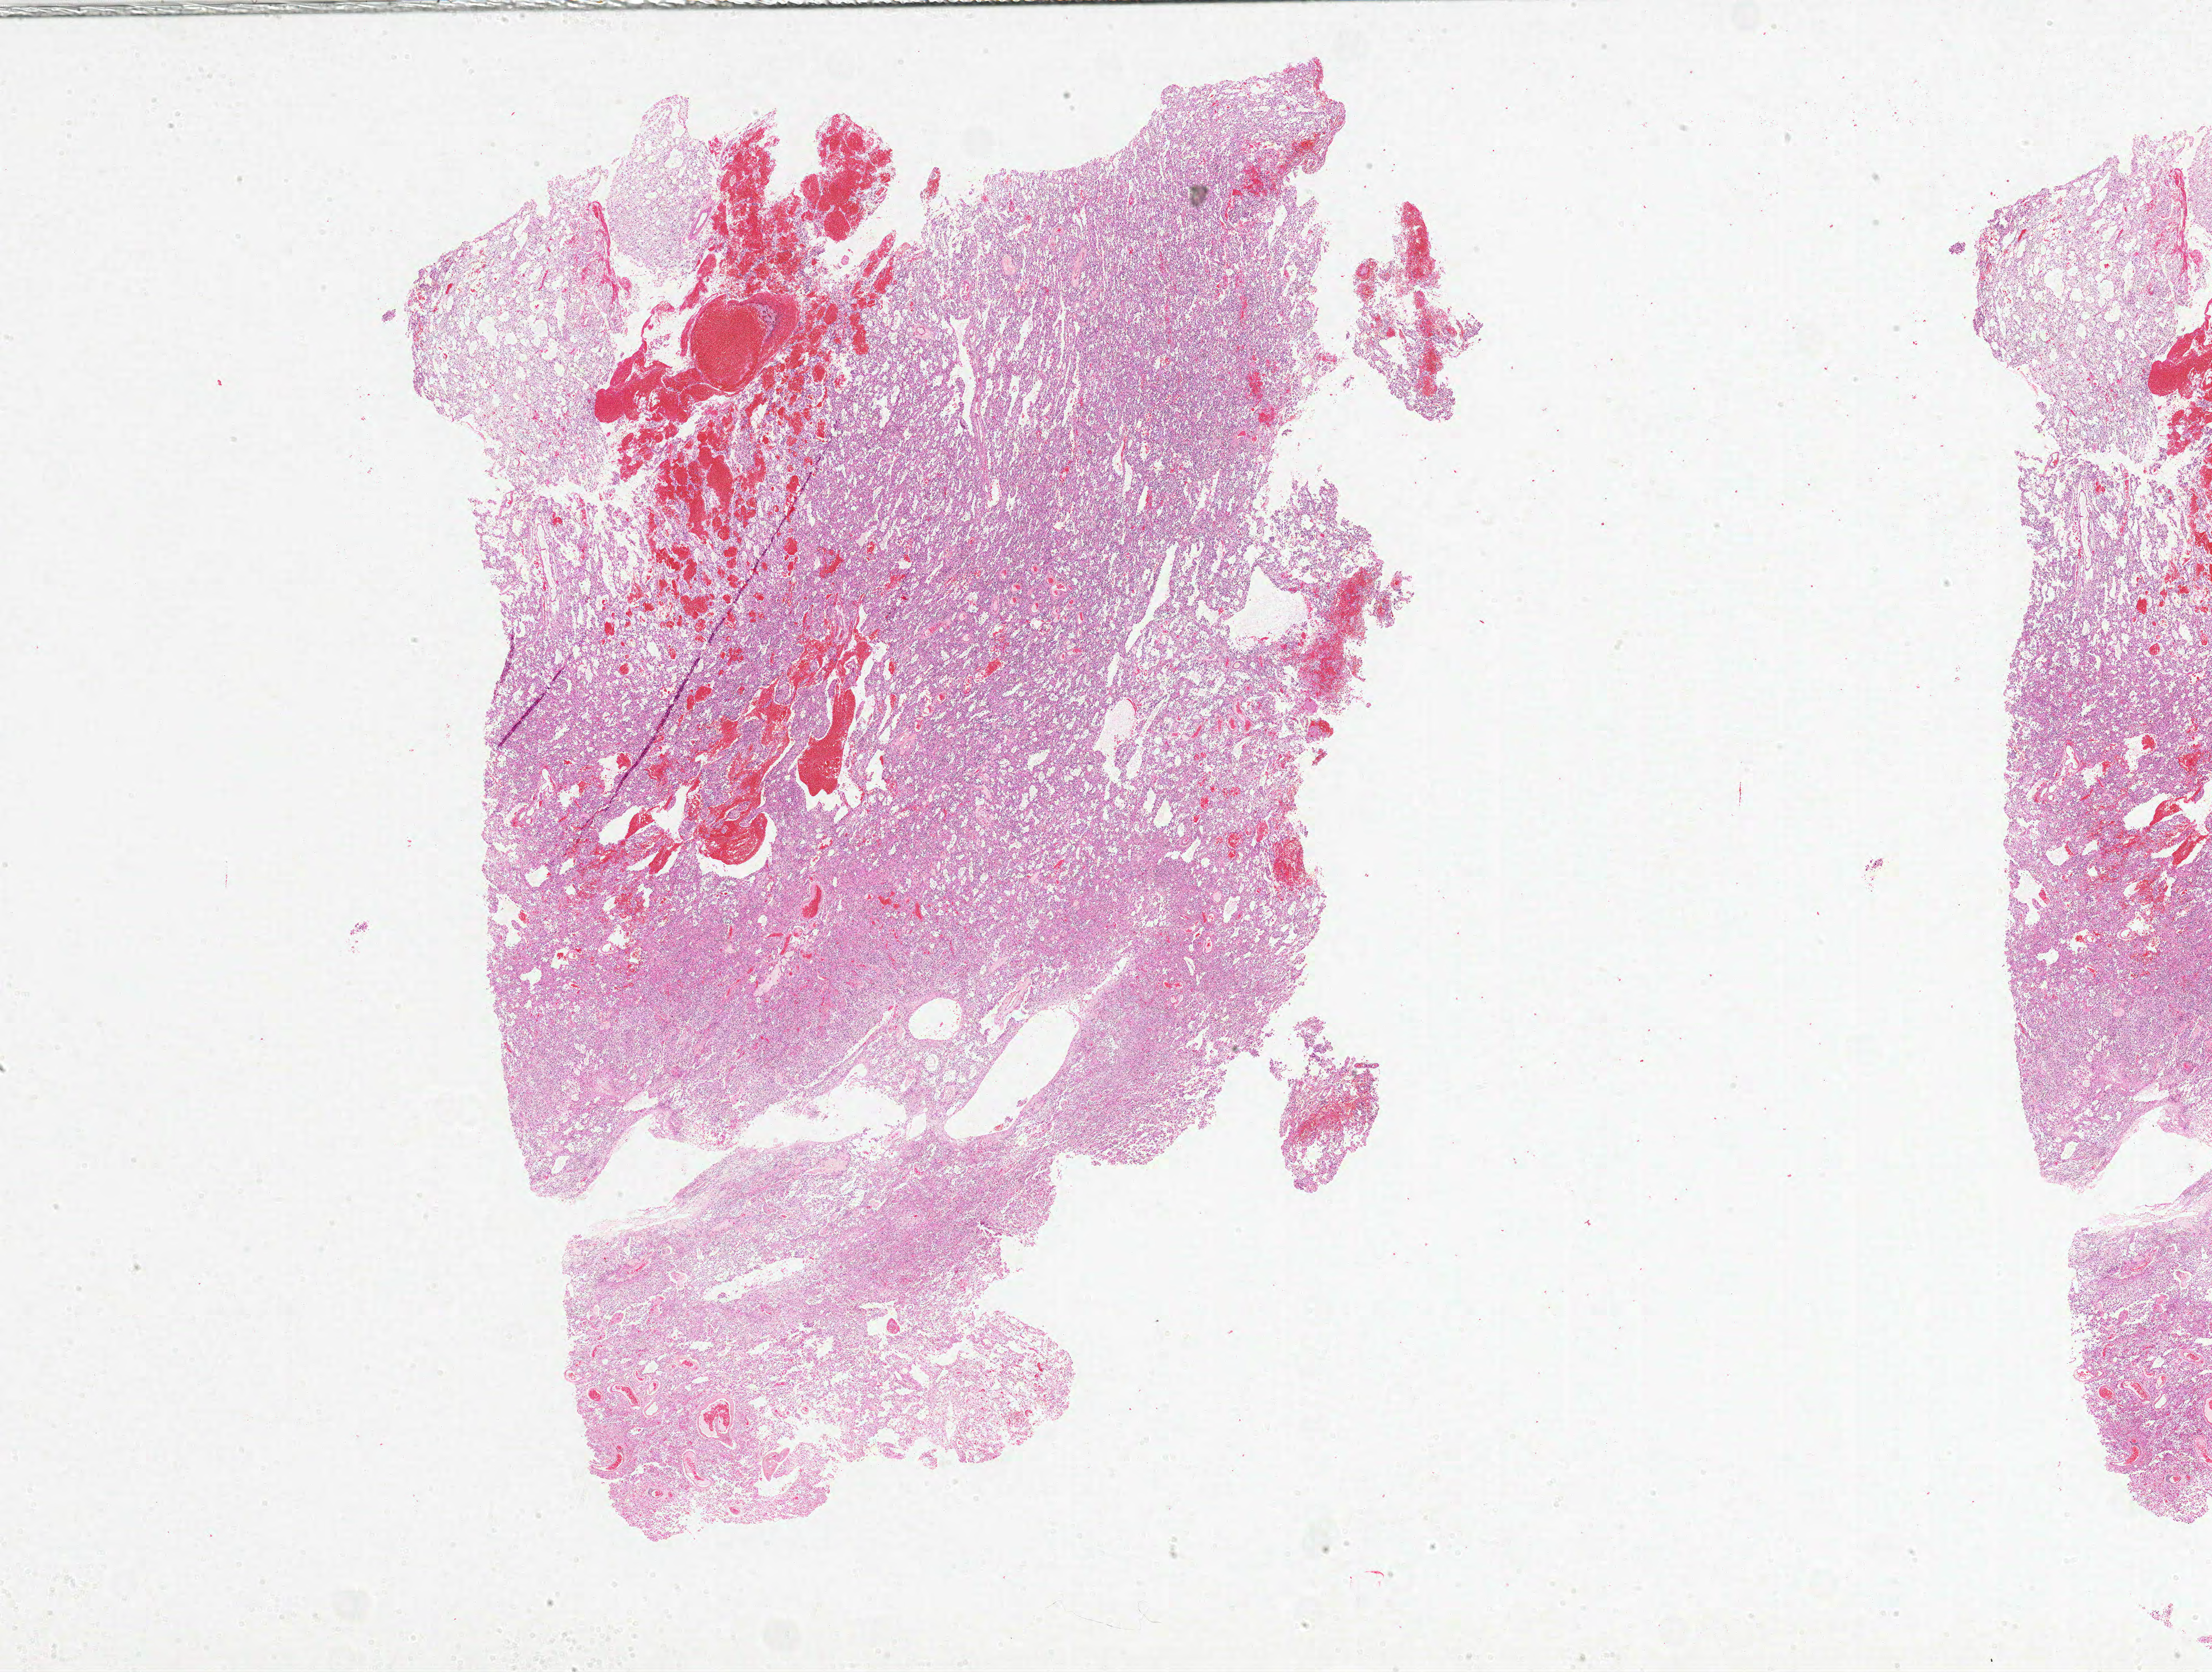
Hematoxylin and eosin (H&E) stained whole-slide image, shown as a low-resolution overview of the whole scanned area (about 31.0 x 23.4 mm, acquisition: 20x scan), FFPE section, sample: primary tumour, brain. Patient: female, age at initial diagnosis 45 years.
Histologic diagnosis: Glioblastoma.